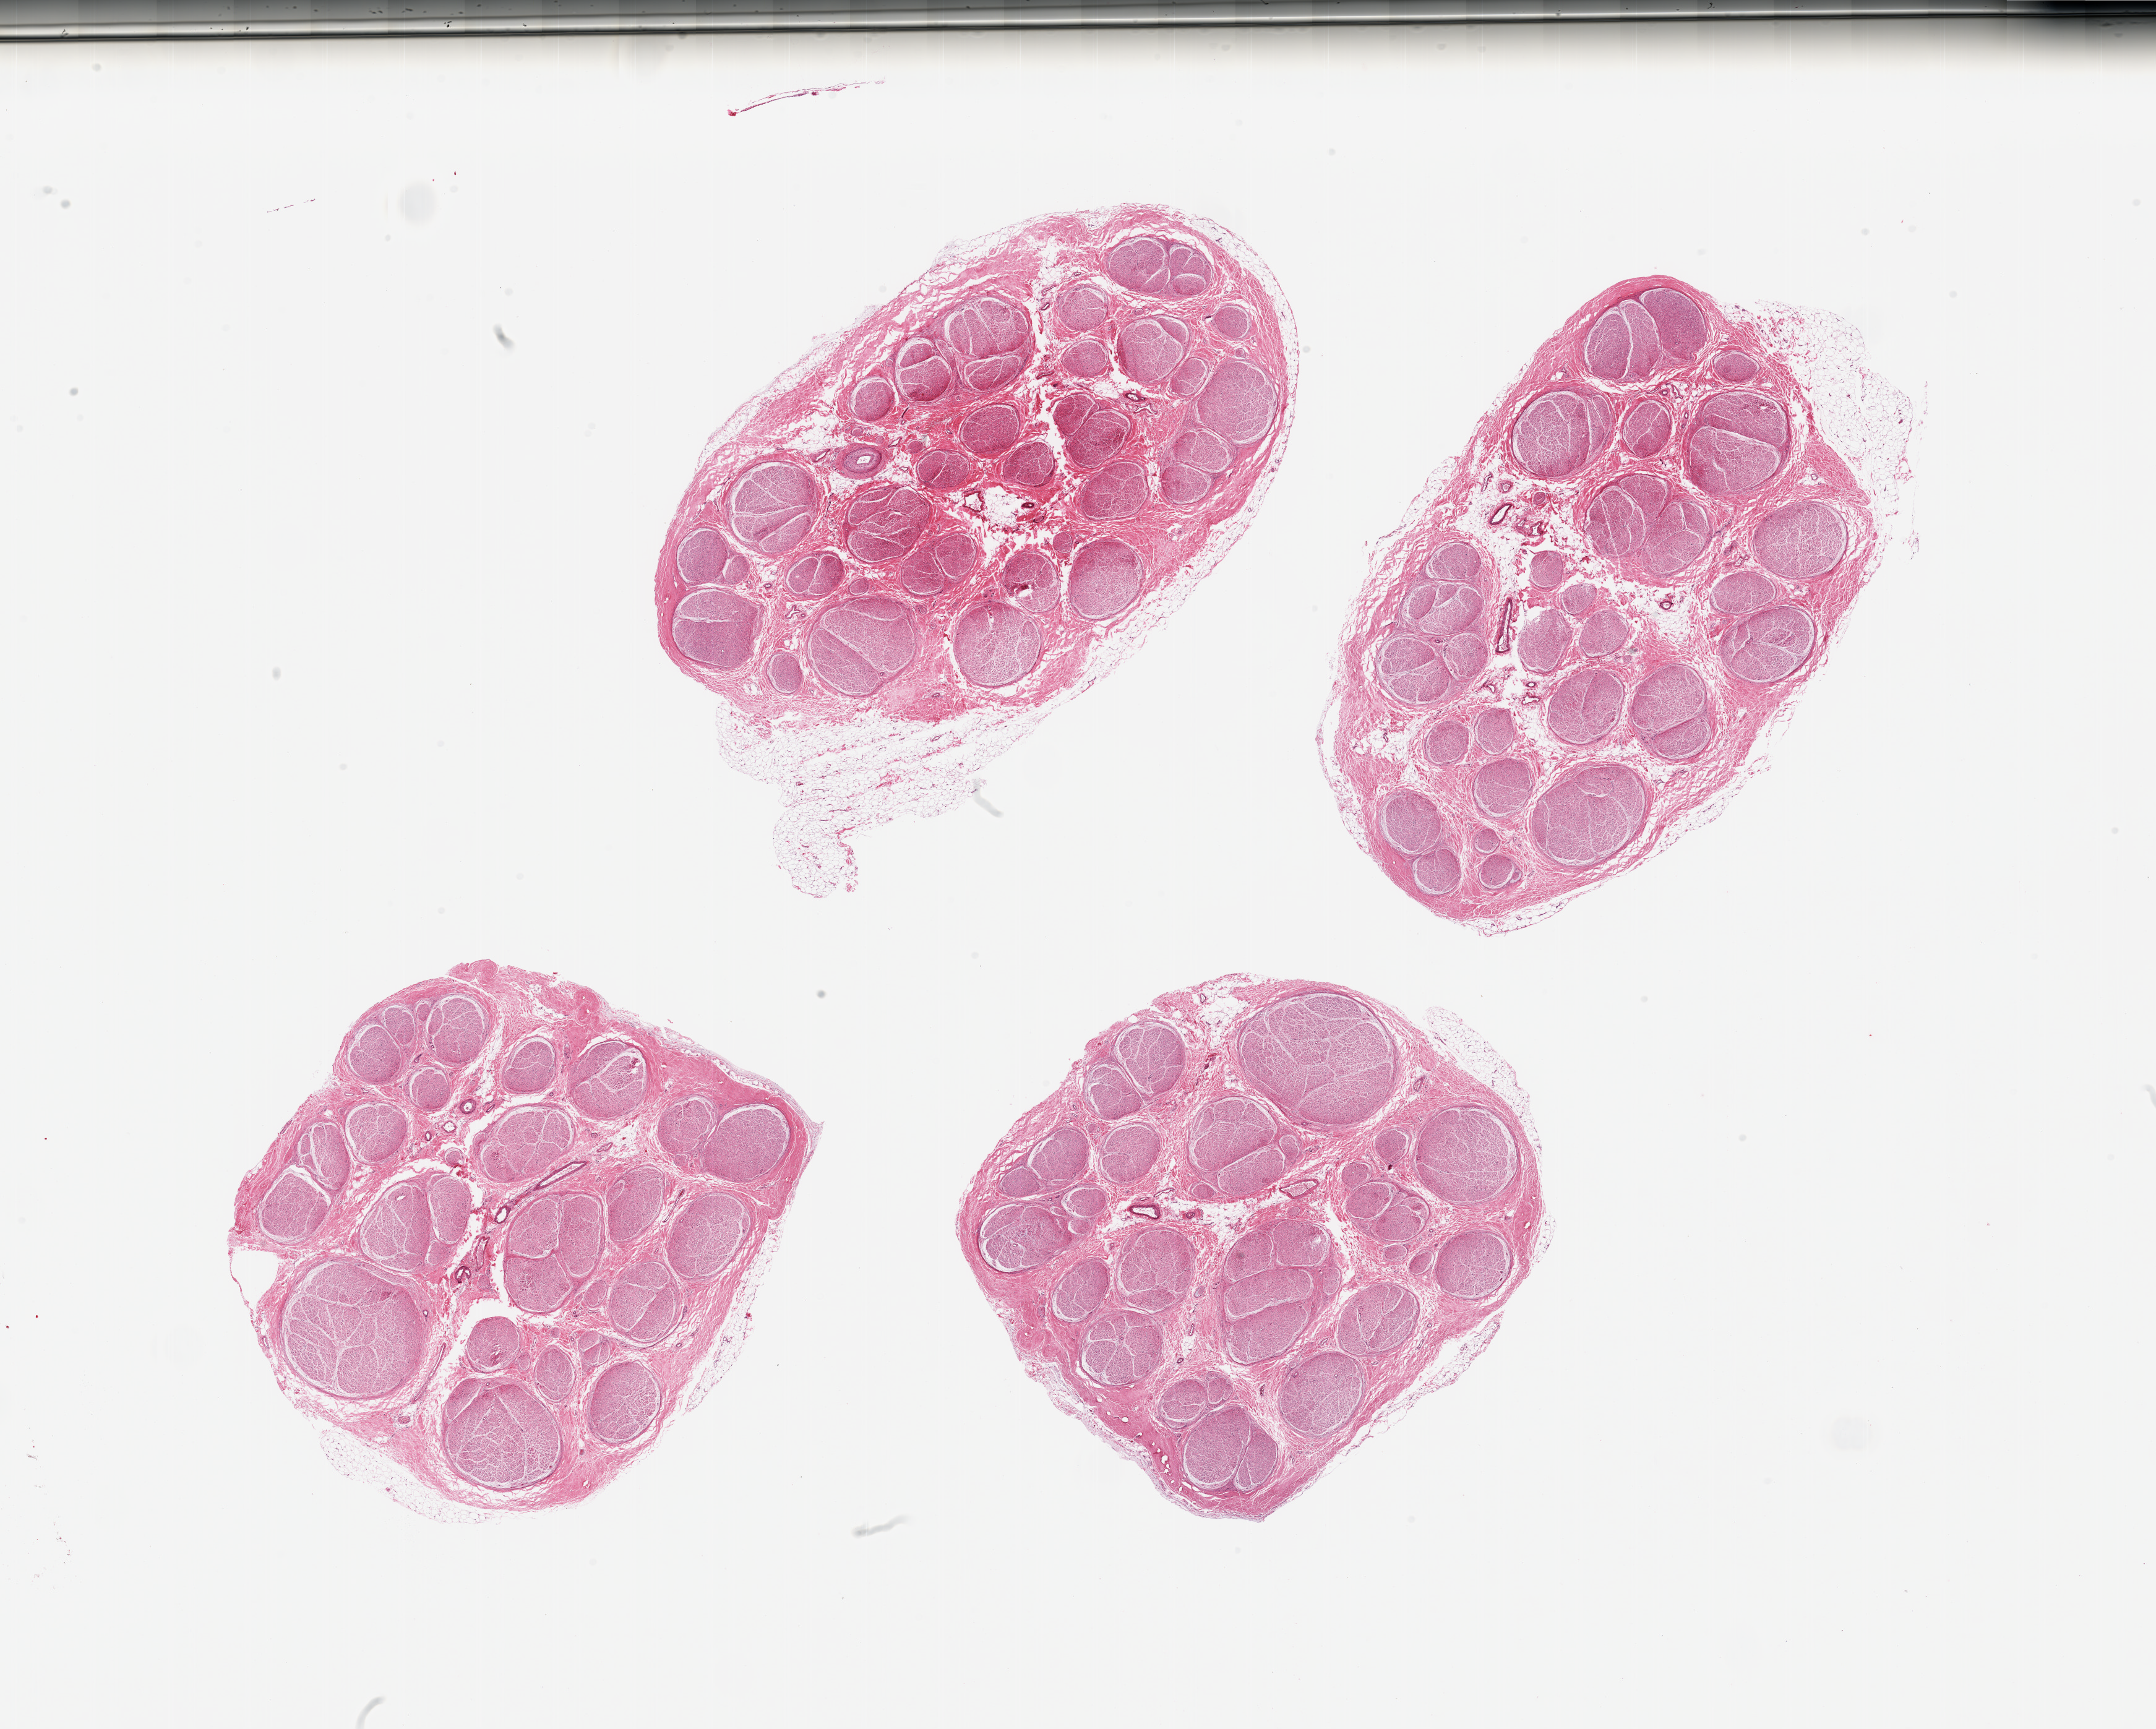
H&E whole-slide image — whole scanned area (about 27.6 x 22.1 mm) shown as a low-resolution overview; PAXgene-fixed, paraffin-embedded tissue; target tissue: tibial nerve; donor tissue sample.
Reviewer comment on this tissue sample: 4 pieces; well trimmed; <10% internal fat.